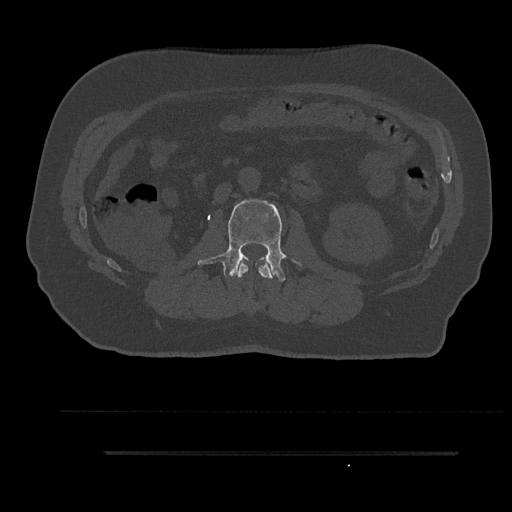
CT including the spine, one axial slice; slice 123 of 797 in the series (ordered by position); 120 kVp; bone window (W 1800 / L 400 HU); 0.5 mm slice thickness; 512 × 512 image matrix, field of view 432 × 432 mm. Male patient, age 63 years. Case-level facts recorded for this patient, not image findings: primary cancer: renal; vertebrae with lytic lesions (as recorded): T8.
Annotated regions visible in this slice (semi-automatic segmentation, software-assisted and operator-edited):
- L1 vertebra: bounding box (x1, y1, x2, y2) in pixels: (237, 259, 275, 279)
- L2 vertebra: (198, 199, 286, 282)